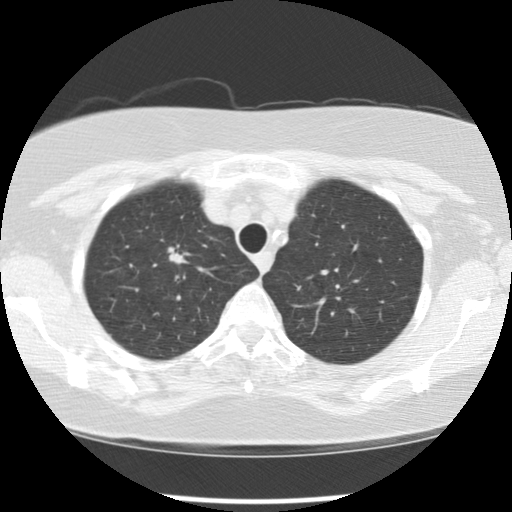
Axial slice from a low-dose chest CT screening exam, baseline annual screen, lung window (W 1500 / L -600 HU), 2.5 mm slice thickness, standard (soft-tissue) reconstruction kernel (STANDARD). Female, age 65 years at enrolment. Current smoker at enrolment.
Lesion marked by an expert reader, bounding box (x1, y1, x2, y2) in pixels: (145, 230, 198, 282). The screening reader recorded 2 non-calcified nodules or masses ≥4 mm on this exam; which of them this box marks is not recorded. Official screen result: positive, change unspecified: nodule(s) >= 4 mm or enlarging nodule(s), mass(es), or other non-specific abnormalities suspicious for lung cancer. Lung cancer was diagnosed 183 days after this screen: large cell carcinoma, NOS, right upper lobe, poorly differentiated (G3), stage IA (AJCC 6th edition), 20 mm at pathology.